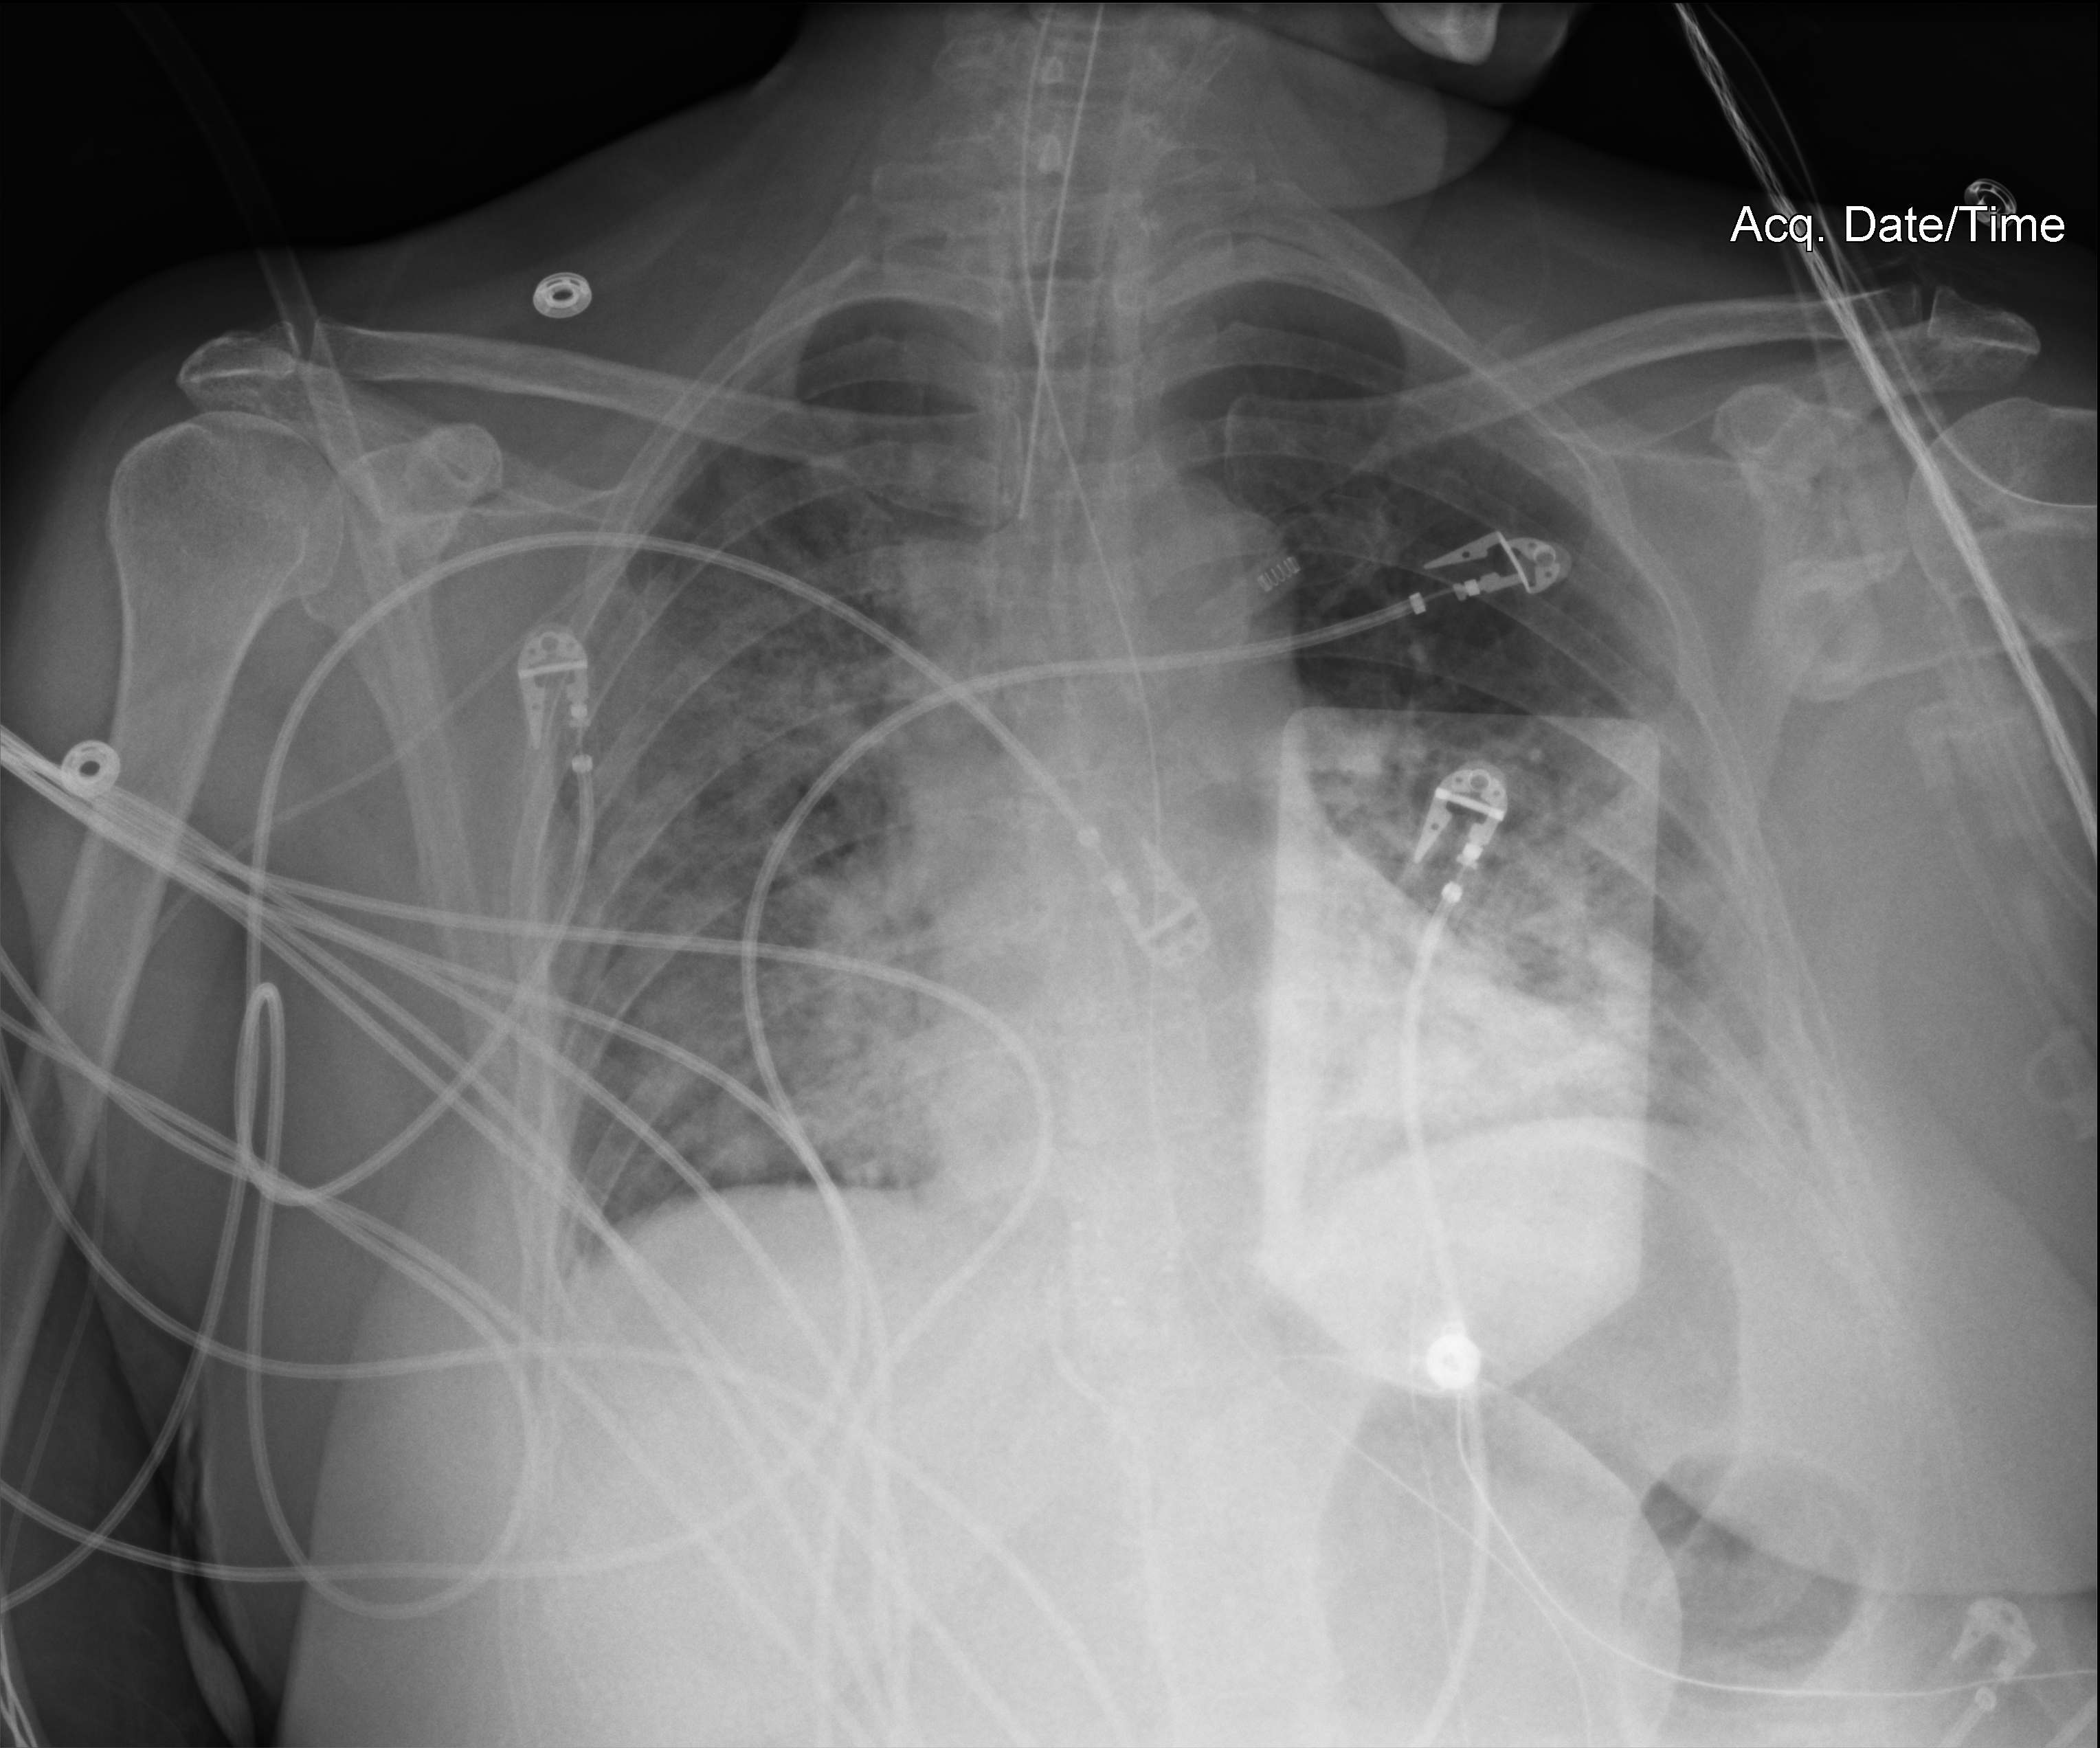
Portable chest radiograph; anteroposterior (AP) projection. Female patient hospitalised with COVID-19, age 18–59 years.
From the hospital-stay record, not from the radiograph (when in the stay this image was taken is not recorded):
- admitted to intensive care during this hospital stay: yes
- diabetes (admission record): yes